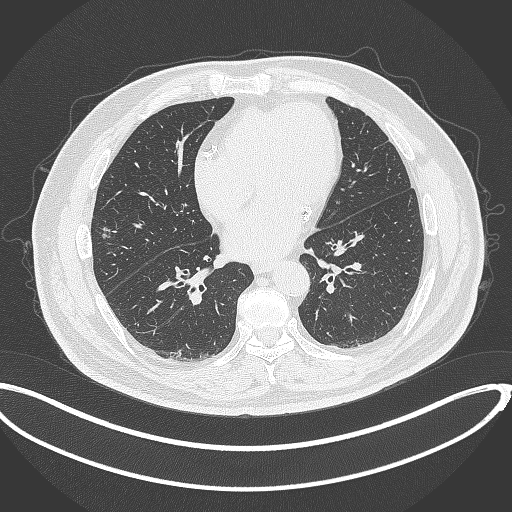
Chest CT, one axial slice. Position 134 of 340 along the scan axis. Reconstruction kernel B70f. 120 kVp. Lung window (W 1500 / L -600 HU). 1 mm slice thickness. 512 × 512 image matrix. Patient: male, 68 years. Case-level facts recorded for this patient, not image findings: clinical TNM (as recorded): T1c N0 M0; histopathological grade: G2.
Annotated regions visible in this slice (bounding box drawn by a radiologist):
- lung tumour (recorded histology: adenocarcinoma): box from (x=98, y=224) to (x=115, y=241) px